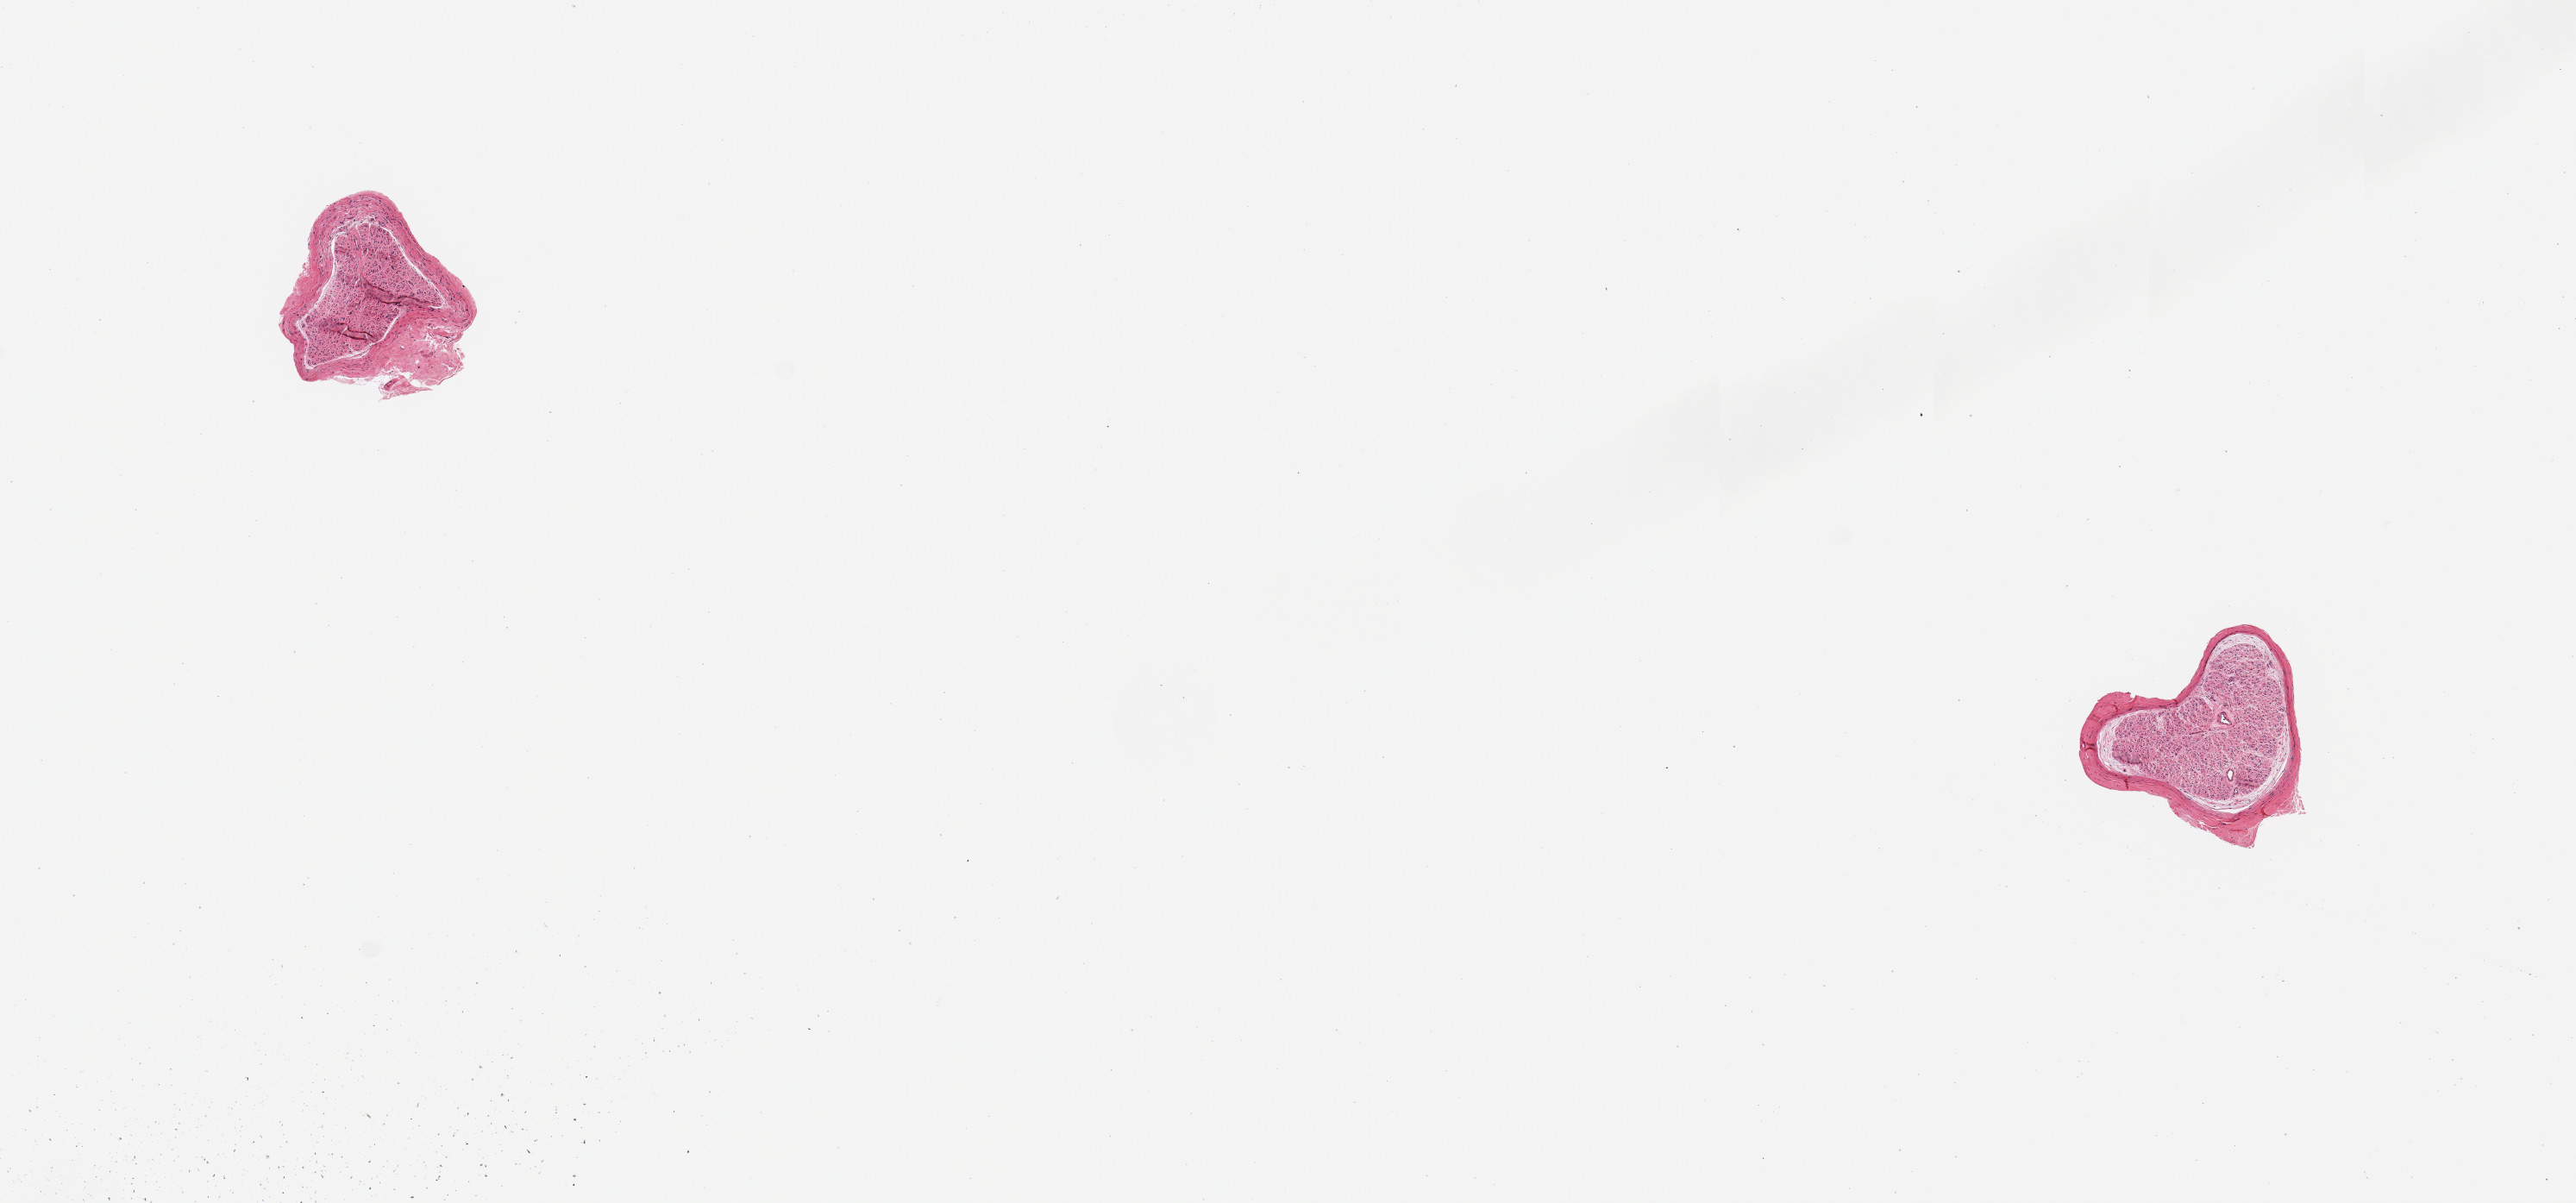
Digitized hematoxylin and eosin (H&E)-stained section, brightfield, shown as a low-resolution overview of the whole scanned area (about 11.8 x 5.5 mm, acquisition: 20x scan), PAXgene-fixed, paraffin-embedded tissue, target tissue: tibial artery, tissue donor sample.
Reviewer comment on this tissue sample: 2 pieces; nerve, not artery.